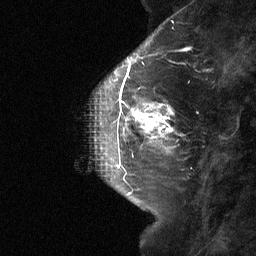
Breast MRI (dynamic contrast-enhanced), one sagittal slice. Slice 18 of 64 in the series (ordered by position). Dynamic contrast-enhanced study with each time point stored as its own series, time point 2 of 3 at this slice position (early post-contrast, ordered by acquisition time). 1.5 T. TE 4.8 ms, TR 27 ms. 2 mm slice thickness. 256 × 256 image matrix, field of view 180 × 180 mm. Female patient, age 42 years. Case-level facts recorded for this patient, not image findings: setting: breast cancer imaged before/during neoadjuvant chemotherapy; receptor status: triple-negative.
Structures marked on this image (semi-automatic segmentation, software-assisted and operator-edited):
- analysis volume of interest (the breast-tissue region the enhancement analysis was run in; not a lesion): bounding box [x1, y1, x2, y2] px = [115, 85, 173, 160]
- tumour enhancement mask (voxels above the 90 % enhancement threshold inside the analysis volume of interest): [120, 88, 172, 143]